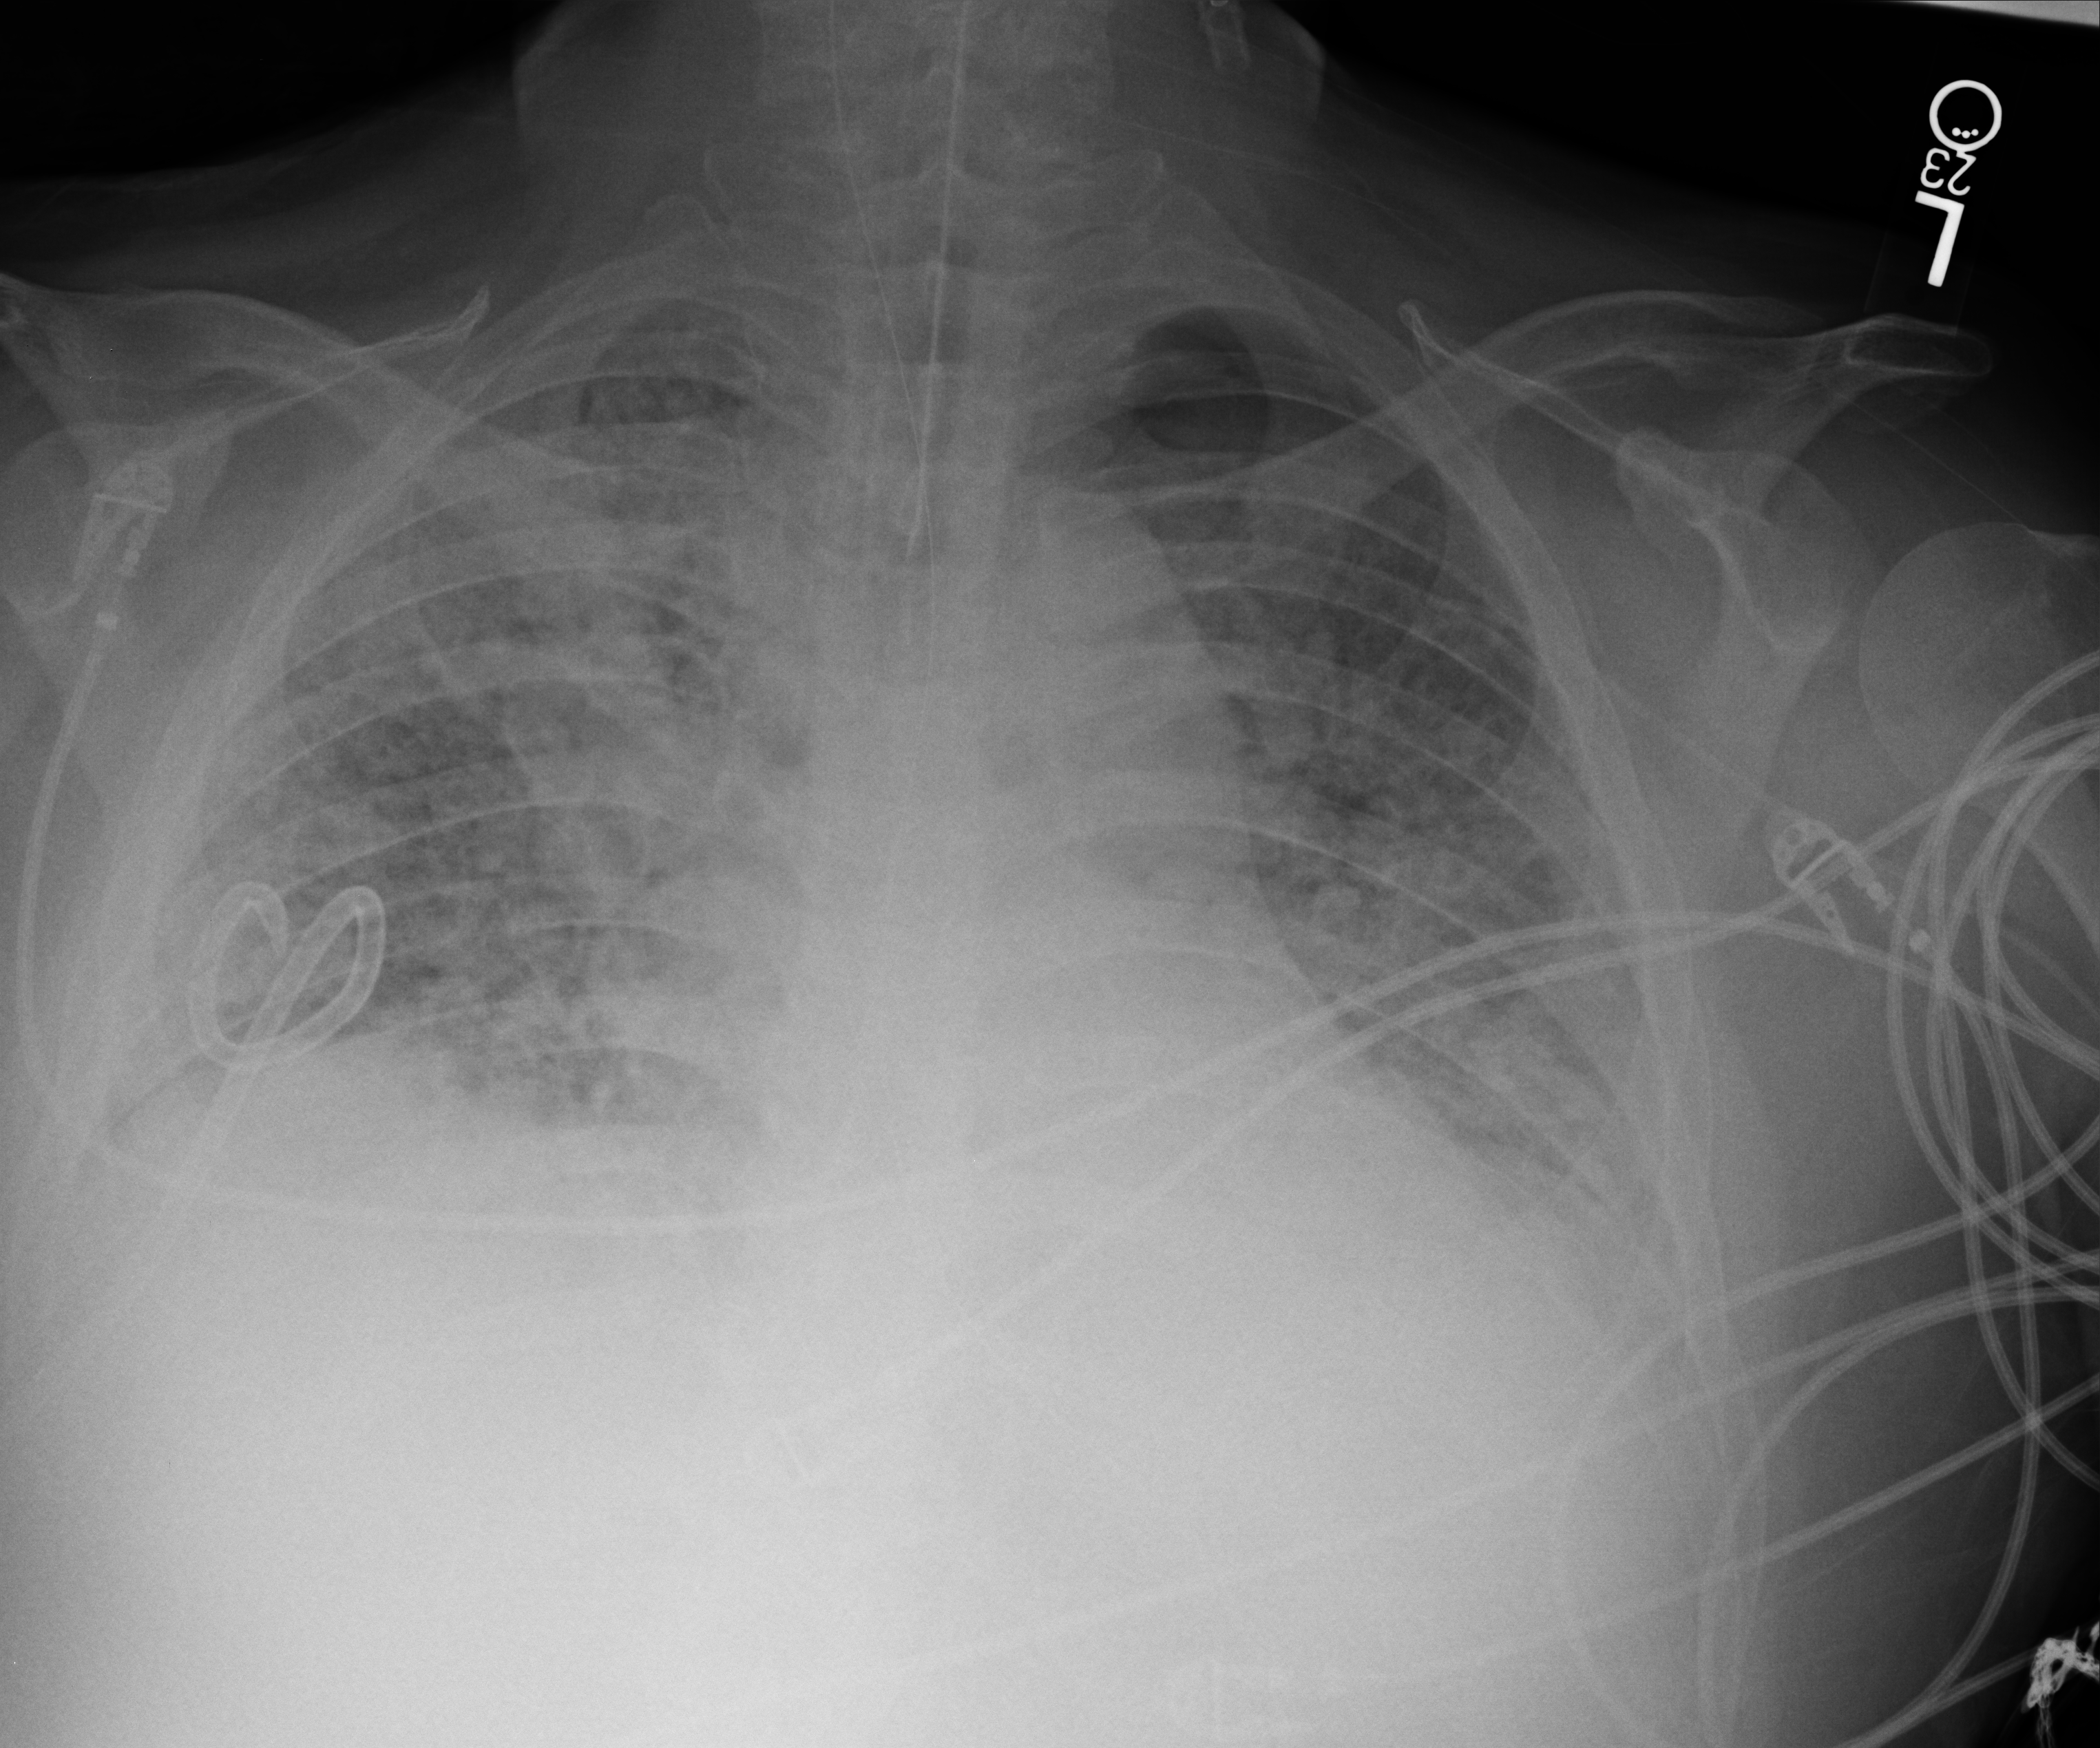
Bedside chest radiograph (computed radiography); anteroposterior (AP) projection. Patient hospitalised with COVID-19, aged 18–59 years.
From the hospital-stay record, not from the radiograph (when in the stay this image was taken is not recorded): mechanically ventilated during this hospital stay: yes; length of hospital stay: 31 days.